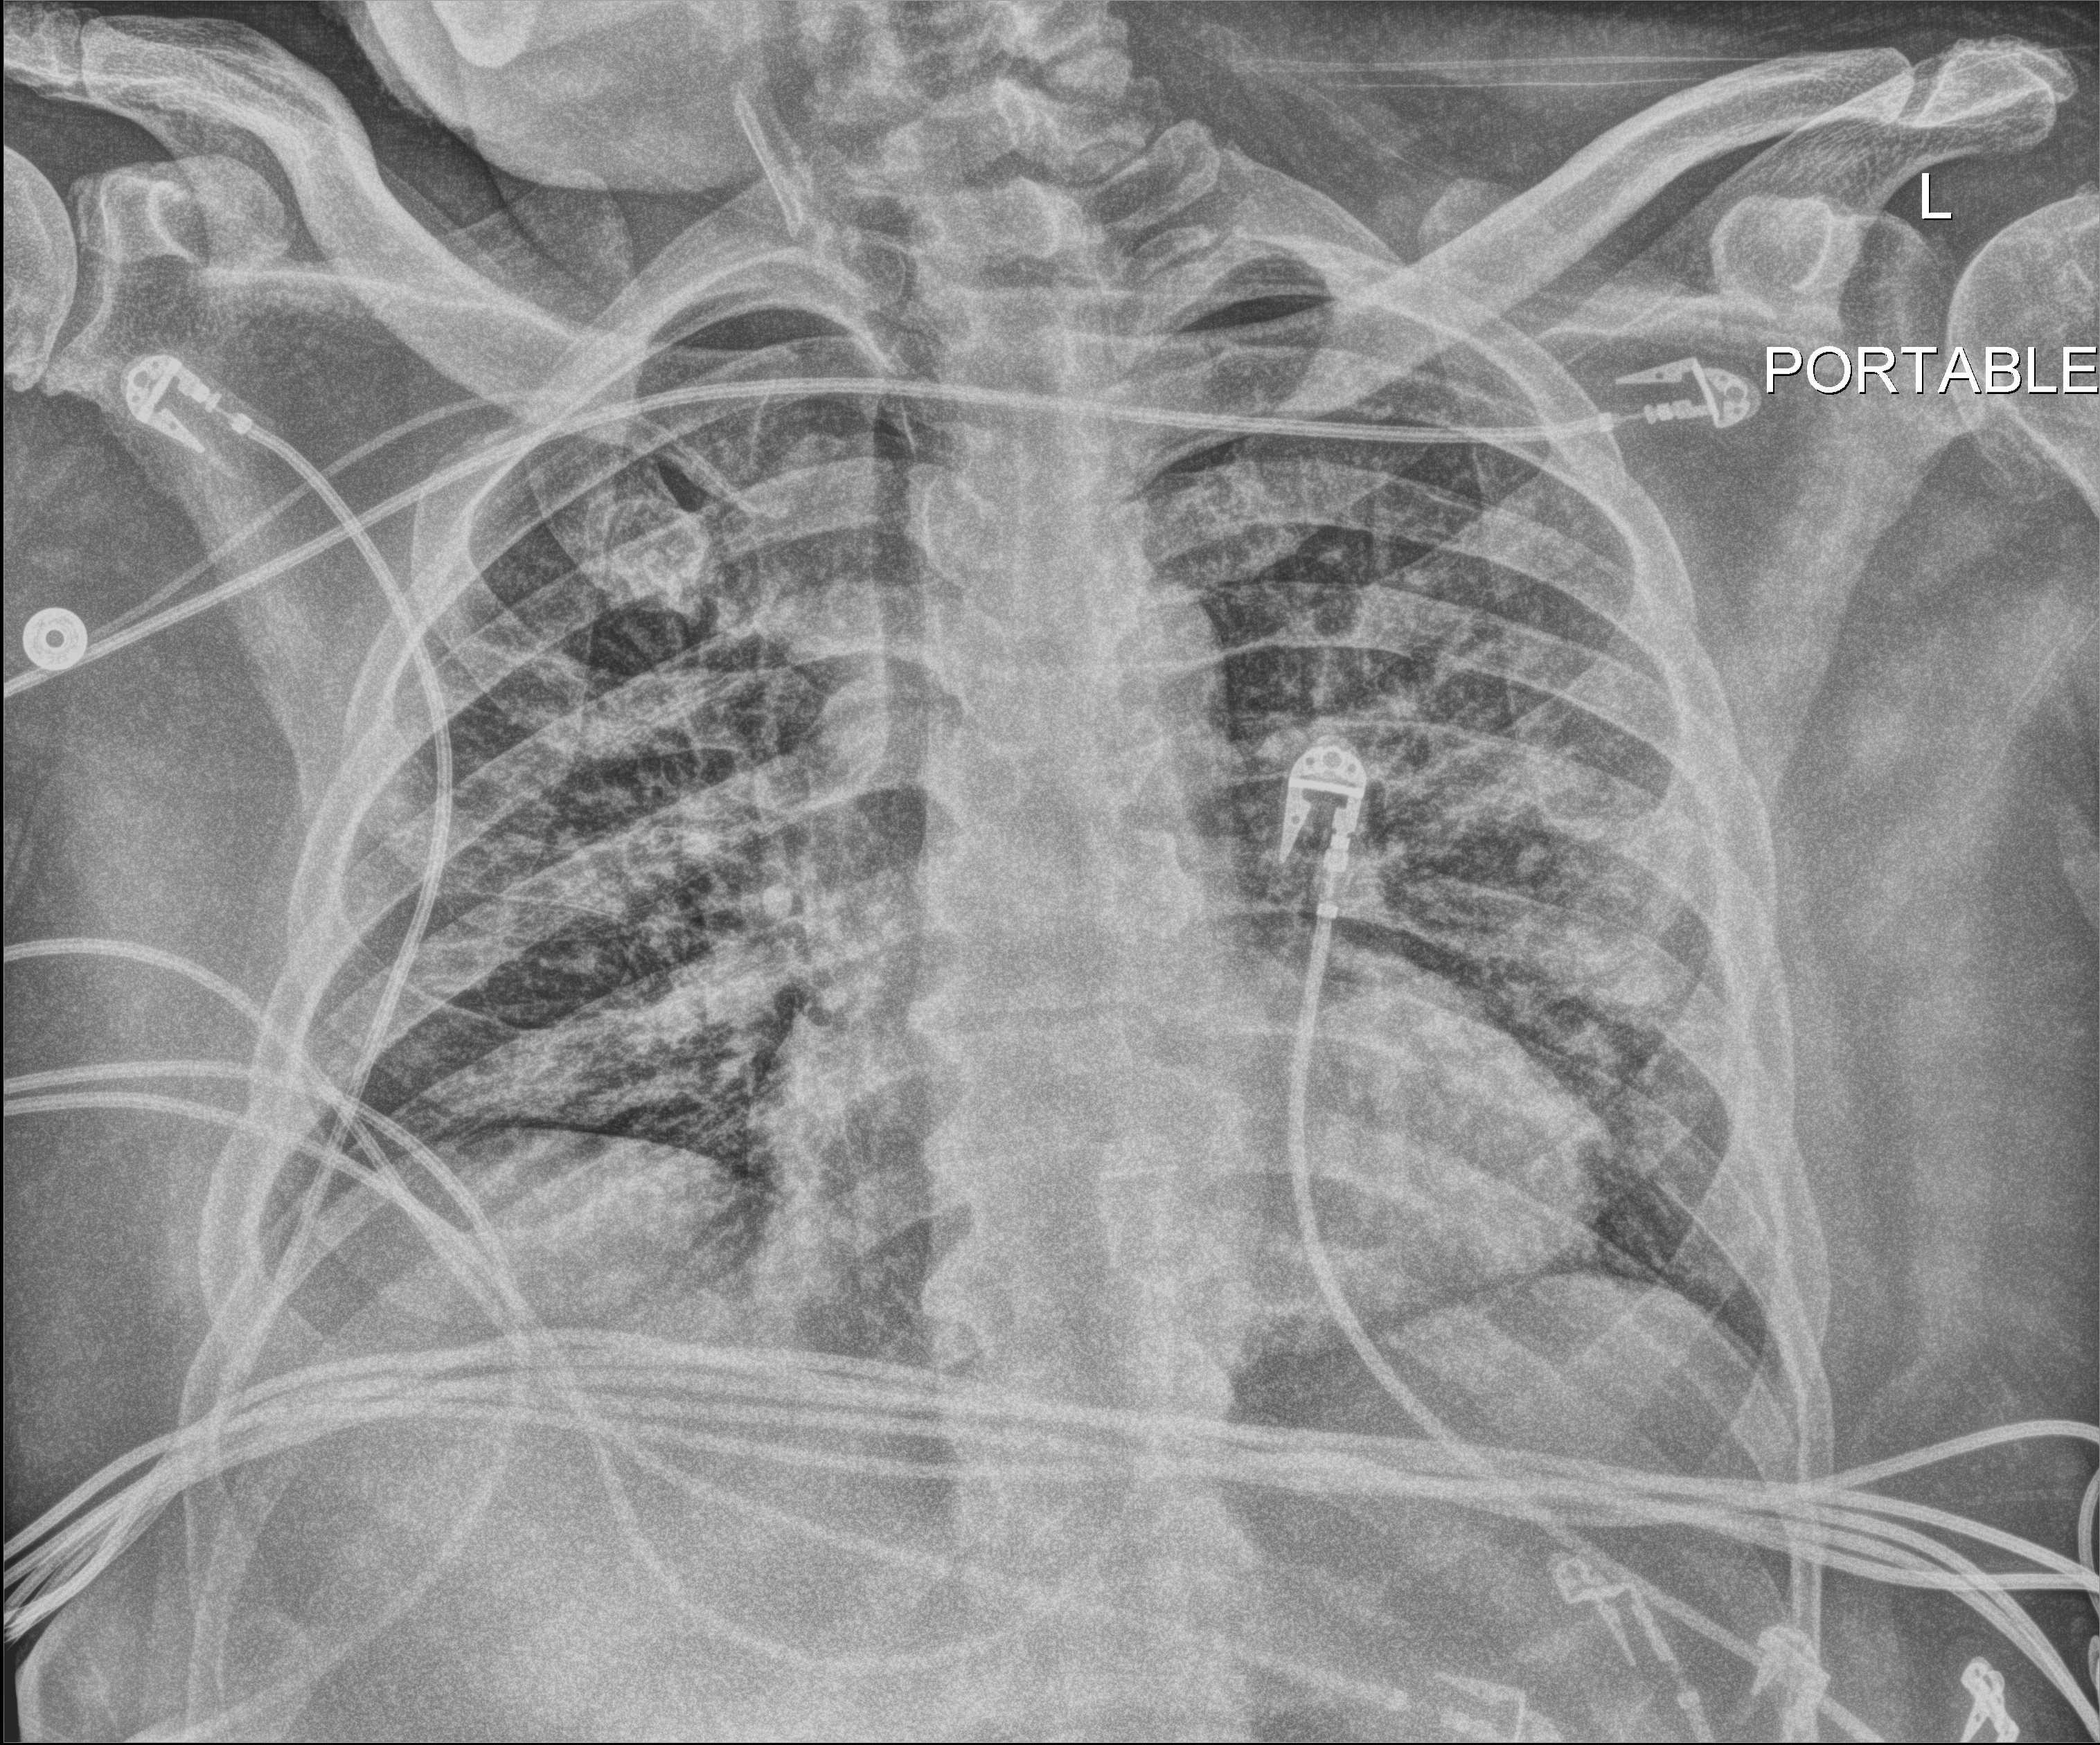
Bedside chest radiograph (digital radiography). Patient hospitalised with COVID-19; male, aged 18–59 years.
Hospital-stay facts (about this admission, not read from this image; timing relative to this image not recorded): length of hospital stay: 41 days; mechanically ventilated during this hospital stay: yes.